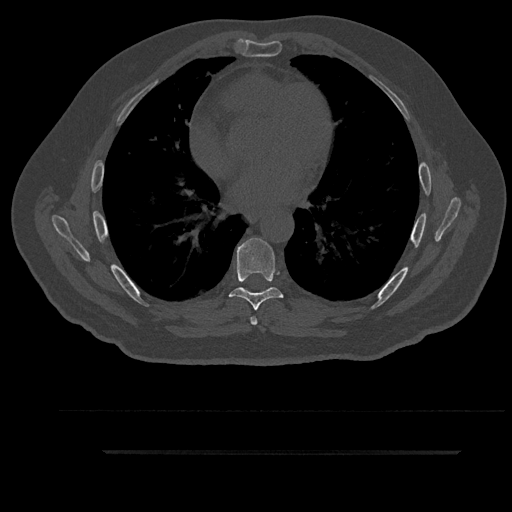
CT including the spine, one axial slice. Position 529 of 797 along the scan axis. Reconstruction kernel Br40s/3. 120 kVp. Bone window (W 1800 / L 400 HU). 512 × 512 image matrix. Male patient, age 63 years. Case-level facts recorded for this patient, not image findings: primary cancer: renal; vertebrae with lytic lesions (as recorded): T8.
Outlined on this slice (semi-automatic segmentation, software-assisted and operator-edited):
- T6 vertebra: box from (x=250, y=288) to (x=270, y=325) px
- T7 vertebra: (x=229, y=238)–(x=283, y=311)